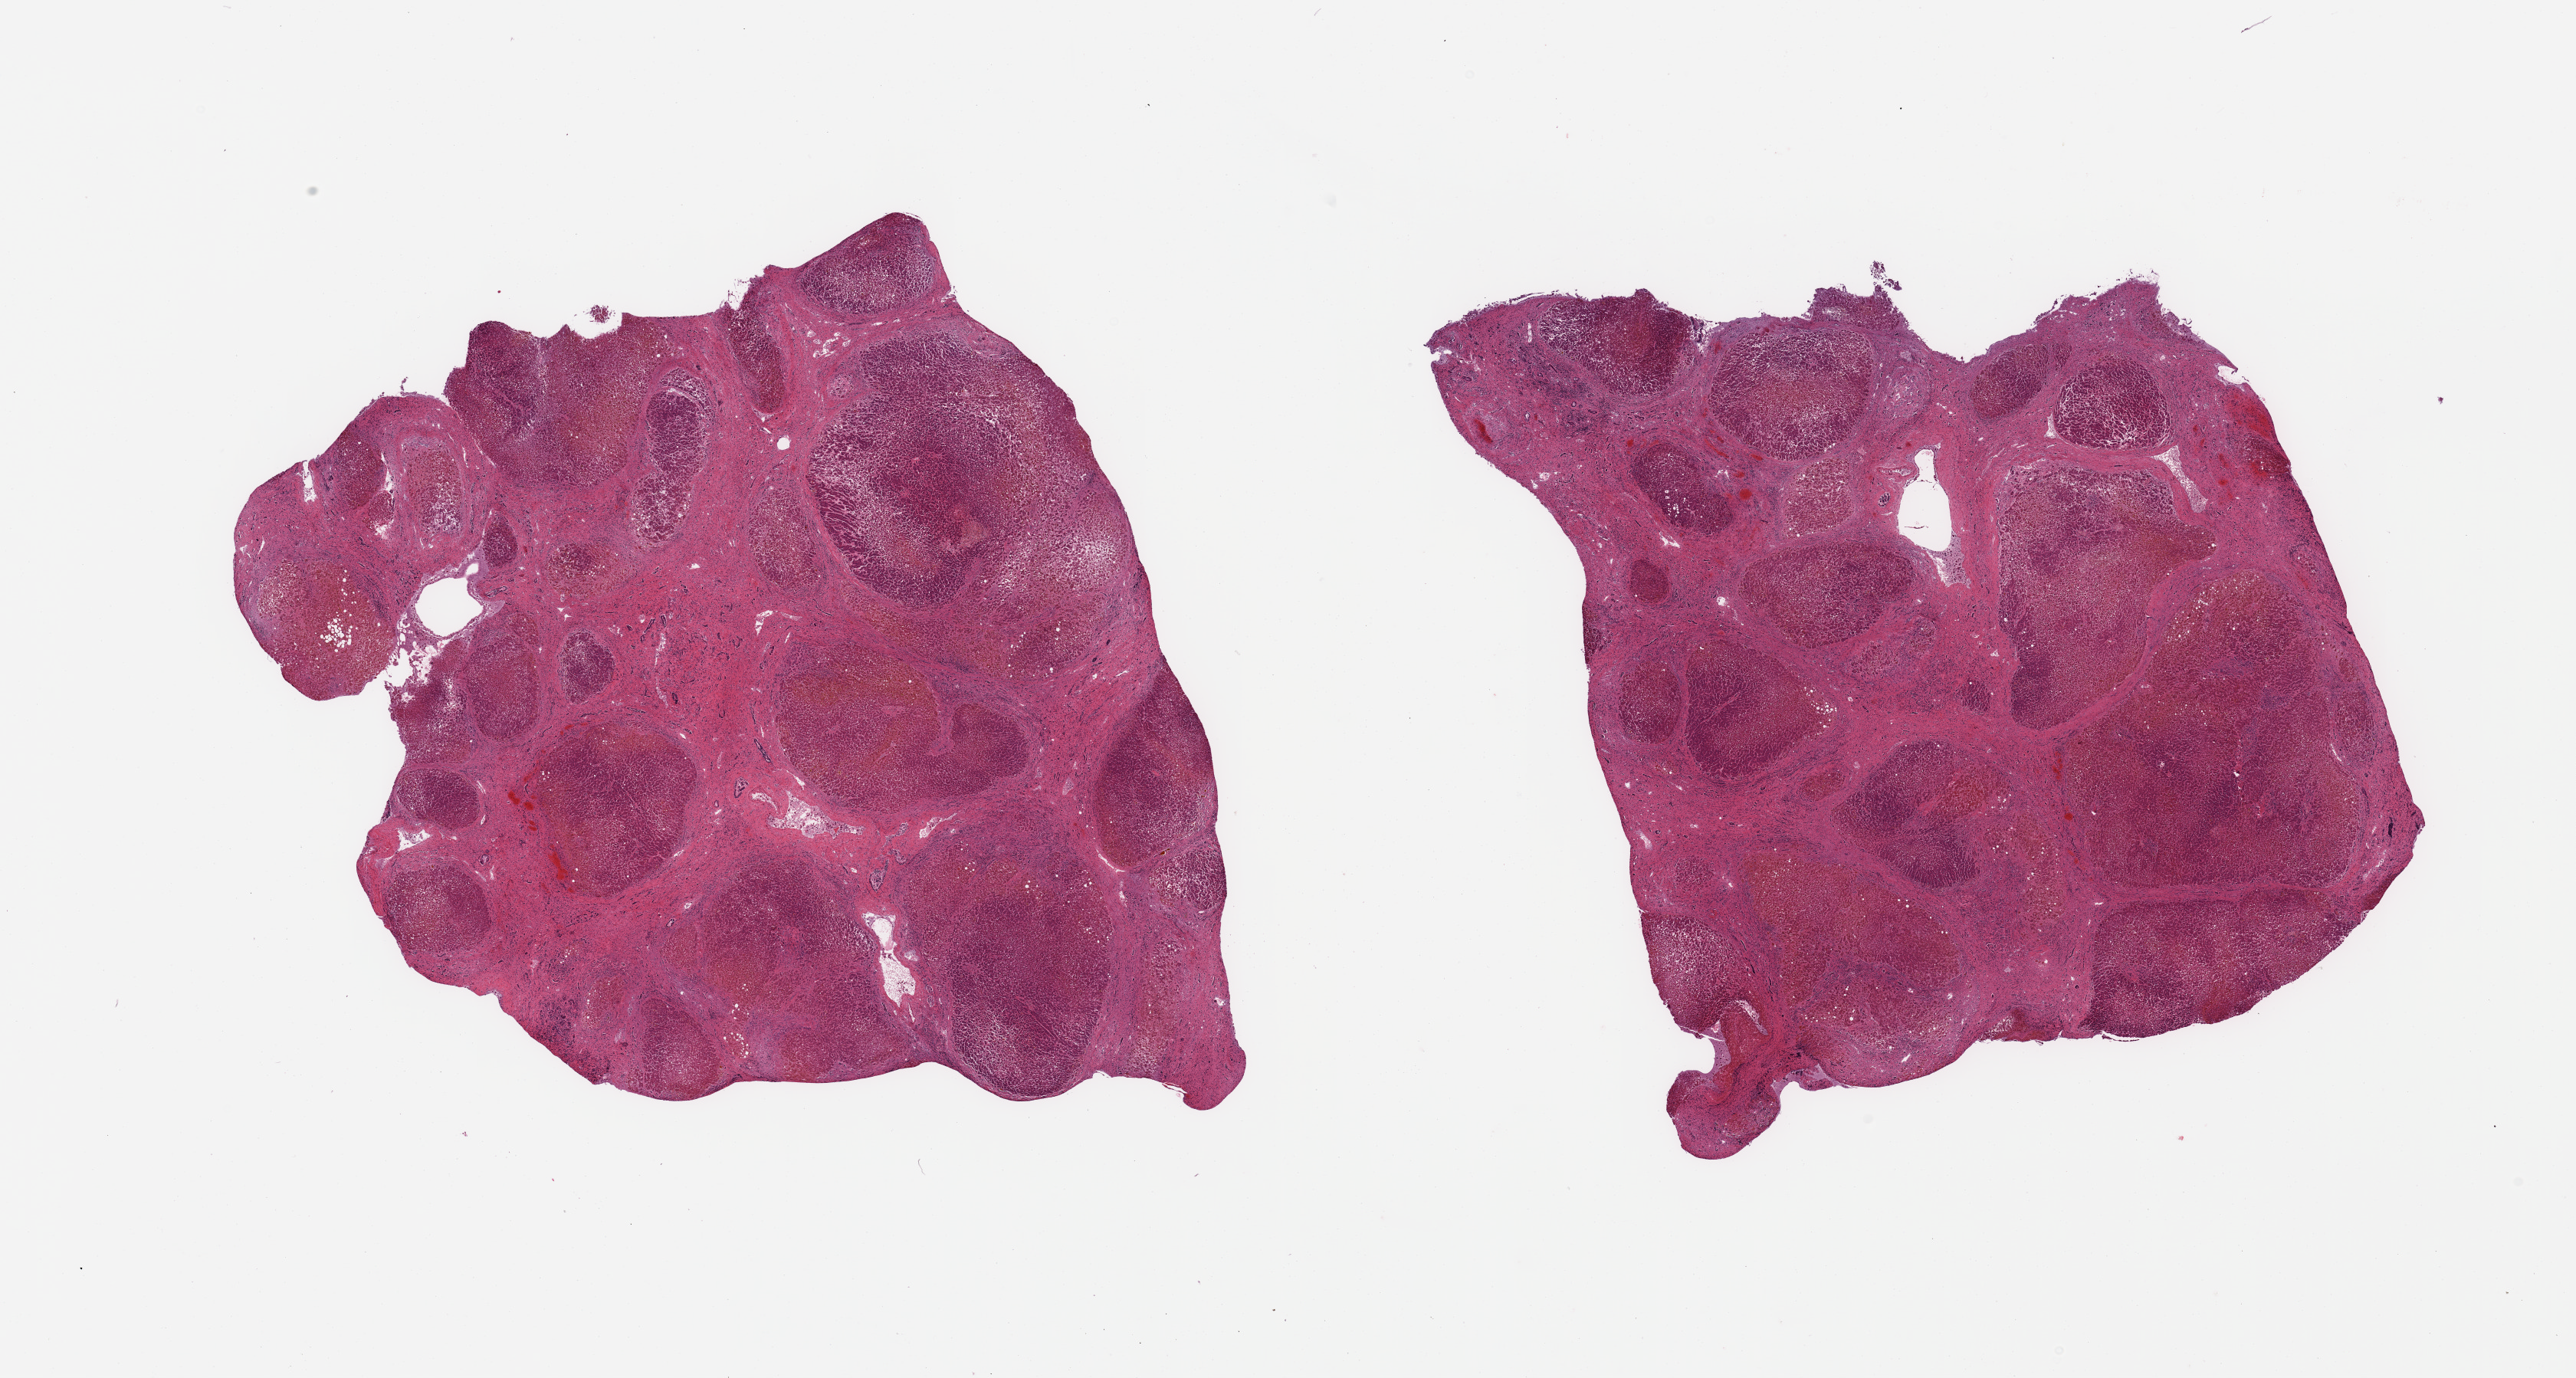
Hematoxylin and eosin (H&E) whole-slide image, a low-resolution overview of the entire scanned area, about 26.6 x 14.2 mm. PAXgene-fixed paraffin-embedded (PFPE) section. Sampled site (target tissue): liver. Donor tissue sample. Donor sex: female.
Reviewer comment on this tissue sample: 2 pieces; nodular cirrhosis; centers of nodules are necrotic; 30% fibrous content; no normal tissue.